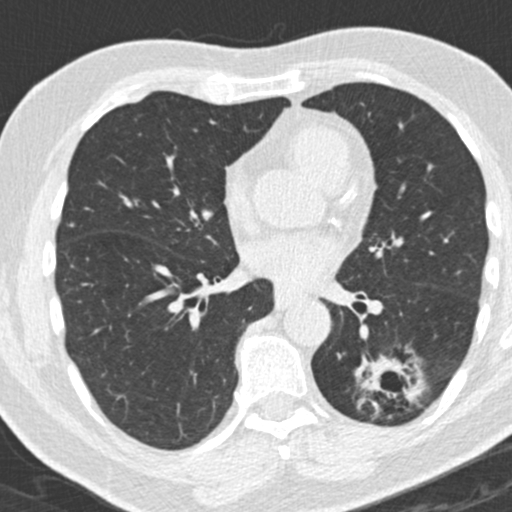
Axial slice from a low-dose chest CT screening exam, third annual screen, lung window (W 1500 / L -600 HU), 2 mm slice thickness, standard (soft-tissue) reconstruction kernel (B30f), slice 88 of 180 in the series, 512 × 512 image matrix. Male, age 66 years at enrolment. Former smoker at enrolment.
Expert reader's lesion annotation, box from (x=356, y=350) to (x=426, y=428) px. The exam's reader record, not a measurement of the box and not confirmed to be the same lesion: non-calcified nodule or mass ≥4 mm, left lower lobe, 31 × 24 mm, spiculated (stellate) margins, pre-existing on the prior screen: yes; interval growth: yes. Official screen result: positive, other. Lung cancer was diagnosed 56 days after this screen: adenocarcinoma, NOS, left lower lobe, poorly differentiated (G3), stage IB (AJCC 6th edition), 38 mm at pathology.